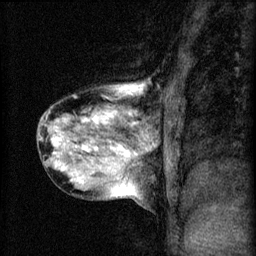
Breast MRI (dynamic contrast-enhanced), one sagittal slice. Slice 25 of 60 in the series (ordered by position). 3 images stored at this slice position (order not interpretable as contrast timing). 1.5 T. TE 4.2 ms, TR 8.2 ms. 2 mm slice thickness. 256 × 256 image matrix, field of view 180 × 180 mm. Female patient, age 40 years.
Structures marked on this image (semi-automatically segmented with operator editing):
- analysis volume of interest (the breast-tissue region the enhancement analysis was run in; not a lesion): box from (x=36, y=80) to (x=167, y=209) px
- tumour enhancement mask (voxels above the 70 % enhancement threshold inside the analysis volume of interest): (x=53, y=86)–(x=144, y=183)